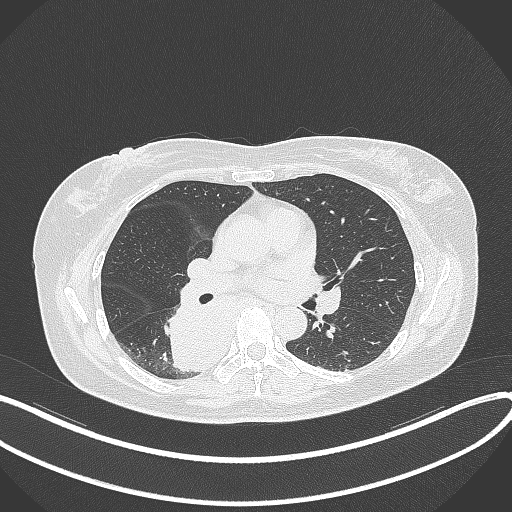
Chest CT, one axial slice; slice 198 of 331 in the series (ordered by position); reconstruction kernel B70f; 120 kVp; lung window (W 1500 / L -600 HU); 512 × 512 image matrix. Female patient, age 54 years. From the clinical record (not read from this slice): clinical TNM (as recorded): T4 N0 M0.
Outlined on this slice (bounding box drawn by a radiologist):
- lung tumour (recorded histology: adenocarcinoma): box from (x=165, y=306) to (x=231, y=372) px